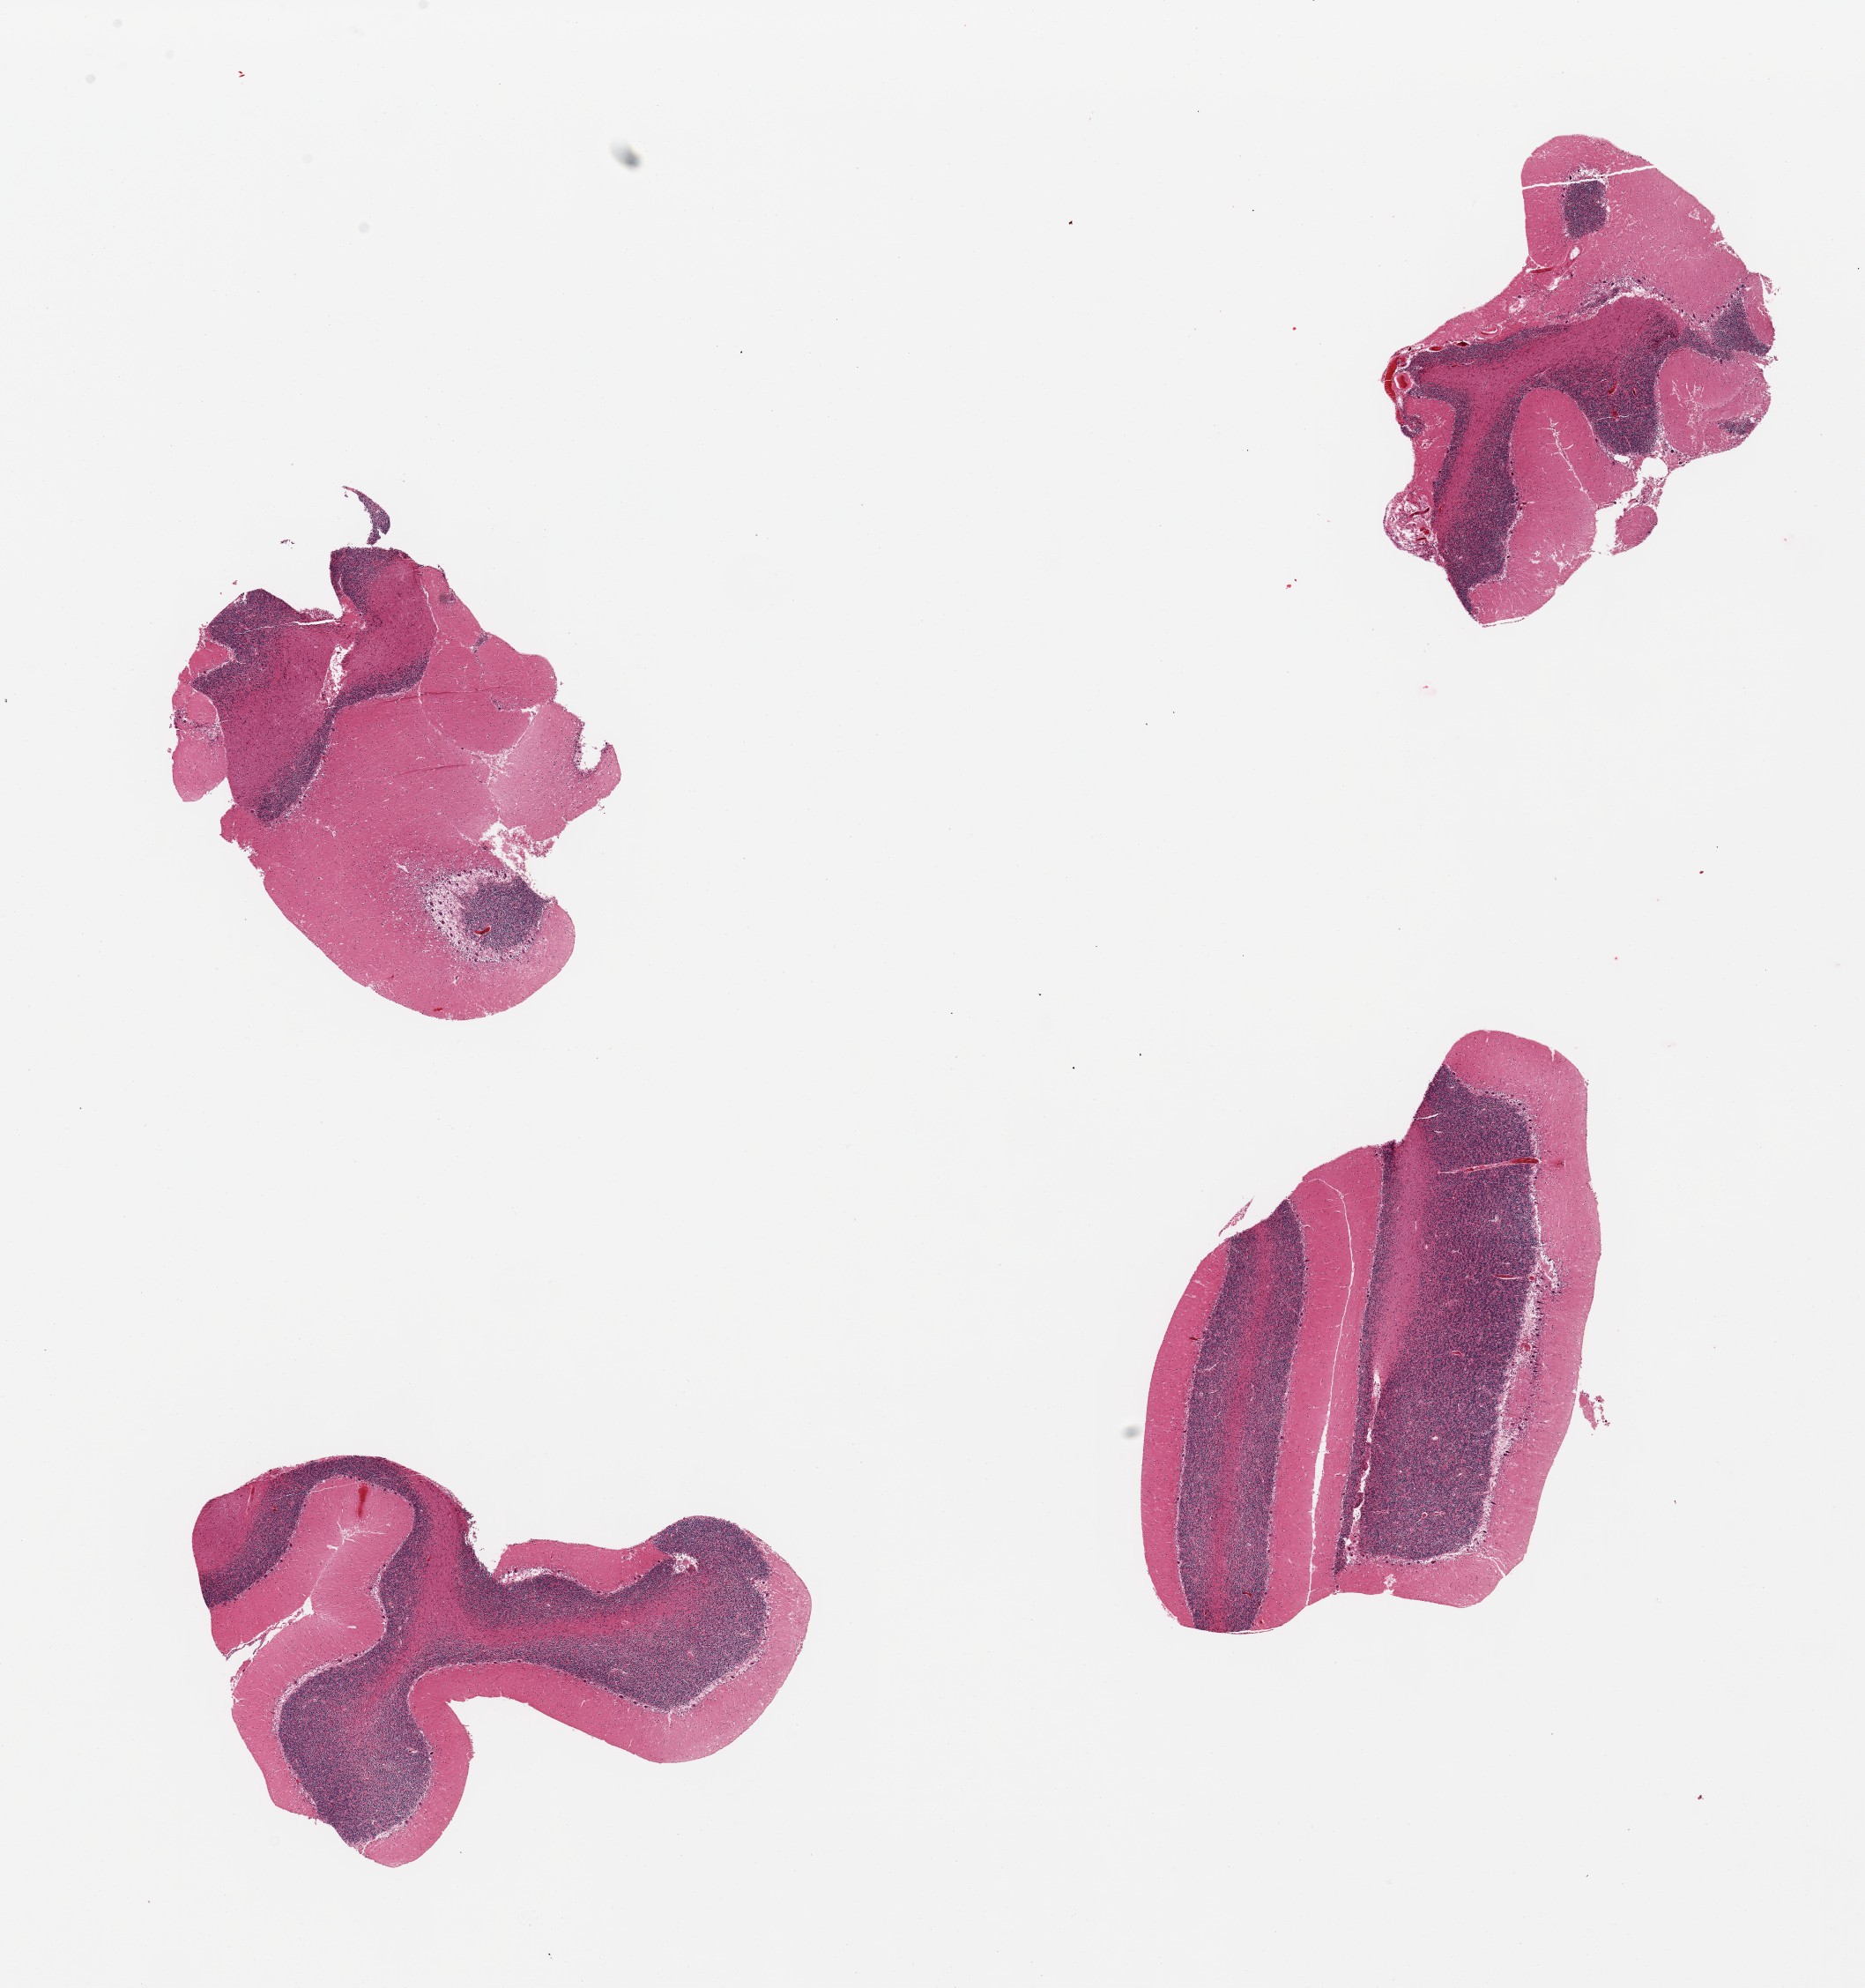
Whole-slide image, haematoxylin and eosin stain — whole scanned area (about 16.7 x 17.8 mm) shown as a low-resolution overview; PAXgene-fixed paraffin-embedded (PFPE) section; target tissue: cerebellum; tissue donor sample. Donor sex: male.
Reviewer comment on this tissue sample: 4 pieces.